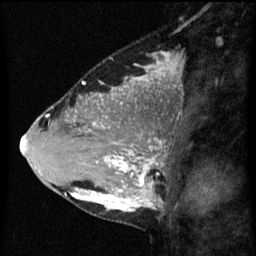
Breast MRI (dynamic contrast-enhanced), one sagittal slice. Slice 24 of 60 in the series (ordered by position). Dynamic contrast-enhanced series, image 2 of 3 at this slice position (ordered by acquisition). 1.5 T. TE 4.2 ms, TR 8 ms. 2.3 mm slice thickness. 256 × 256 image matrix, field of view 180 × 180 mm. Patient: female, 33 years.
Outlined on this slice (semi-automatically segmented with operator editing):
- analysis volume of interest (the breast-tissue region the enhancement analysis was run in; not a lesion): bounding box (x1, y1, x2, y2) in pixels: (71, 118, 170, 215)
- tumour enhancement mask (voxels above the 70 % enhancement threshold inside the analysis volume of interest): (71, 124, 162, 213)